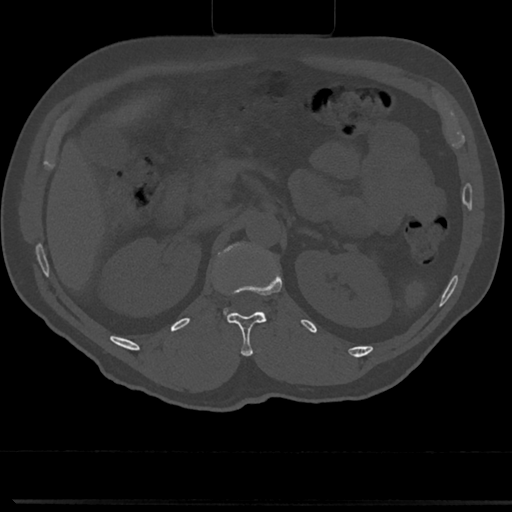
CT including the spine, one axial slice. Reconstruction kernel Br40s/3. Bone window (W 1800 / L 400 HU). 0.5 mm slice thickness. 512 × 512 image matrix, field of view 355 × 355 mm. Male patient, age 61 years. From the clinical record (not read from this slice): primary cancer: prostate.
Annotated regions visible in this slice (semi-automatic segmentation, software-assisted and operator-edited):
- L1 vertebra: box from (x=212, y=241) to (x=275, y=321) px
- T12 vertebra: (x=218, y=284)–(x=267, y=356)